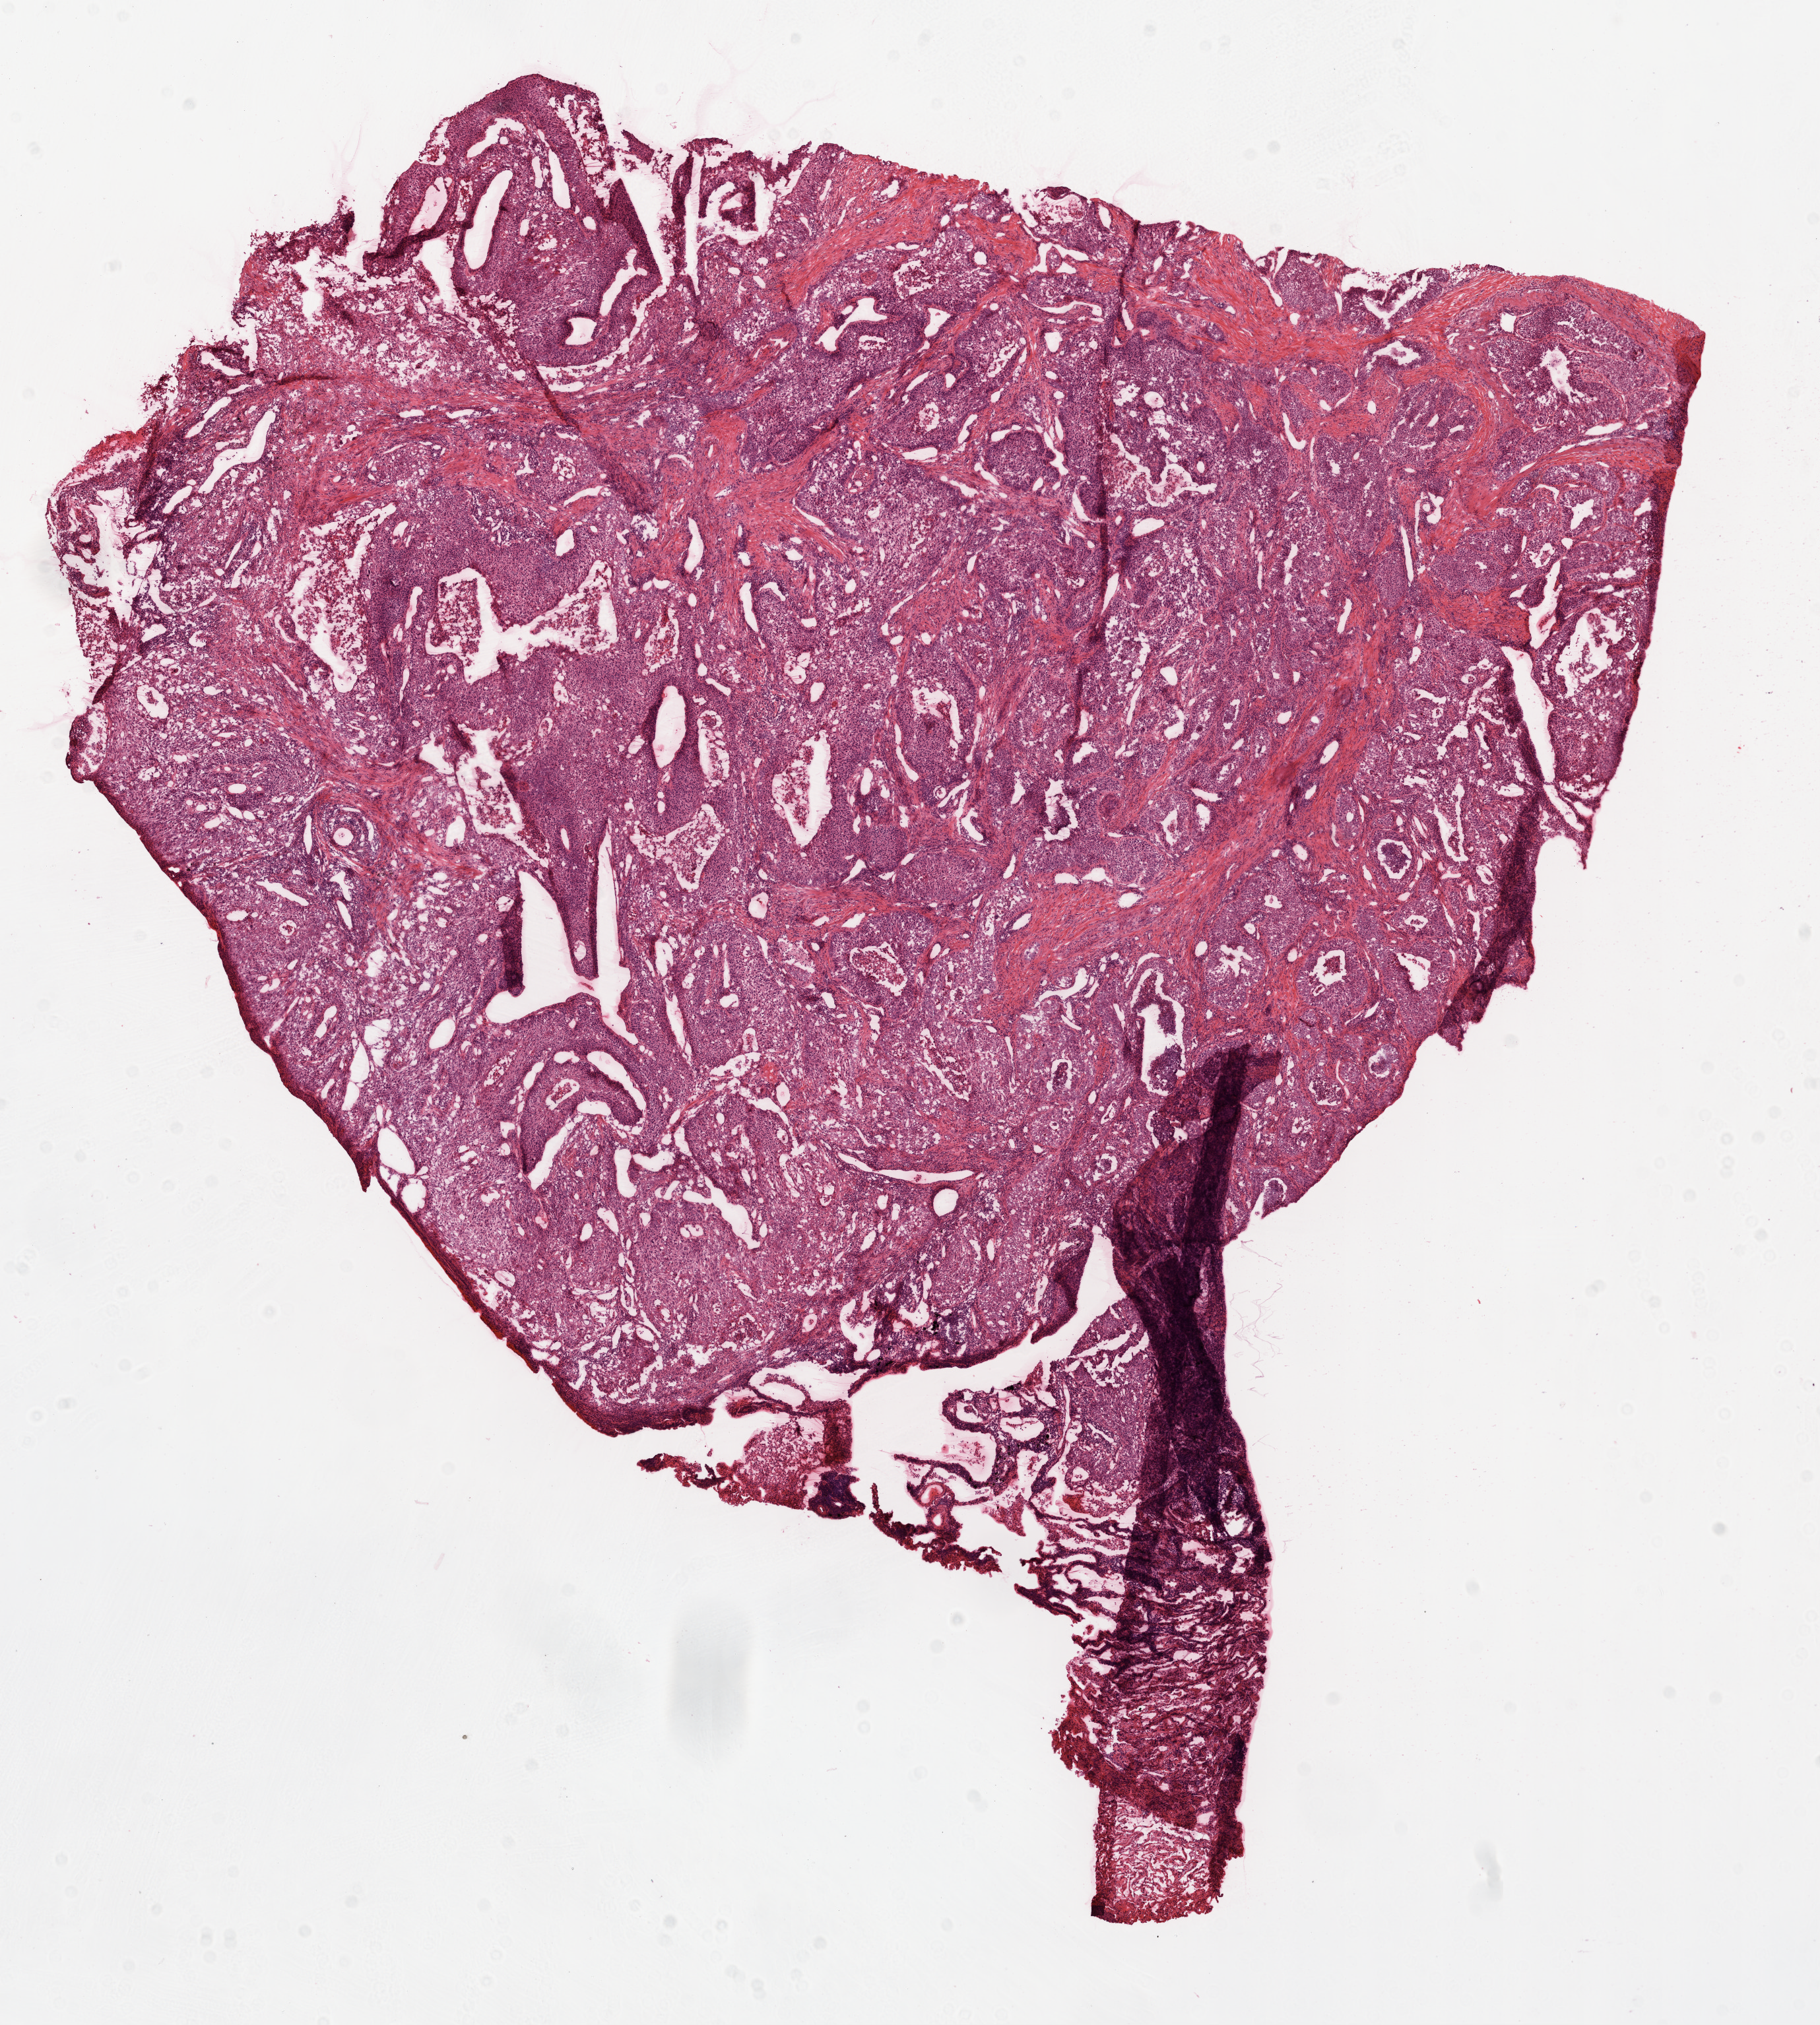
Hematoxylin and eosin (H&E) stained whole-slide image — whole scanned area (about 11.1 x 12.4 mm) shown as a low-resolution overview, frozen section from the top of the tissue portion, primary tumour sample from the lung. Female patient; age at initial diagnosis 60 years. Pathologist review of this section (percent, as recorded): tumour nuclei 95%, necrosis 3%.
Diagnosis: Squamous cell carcinoma, NOS (upper lobe, lung). AJCC pathologic stage: IIIA. Laterality: left.